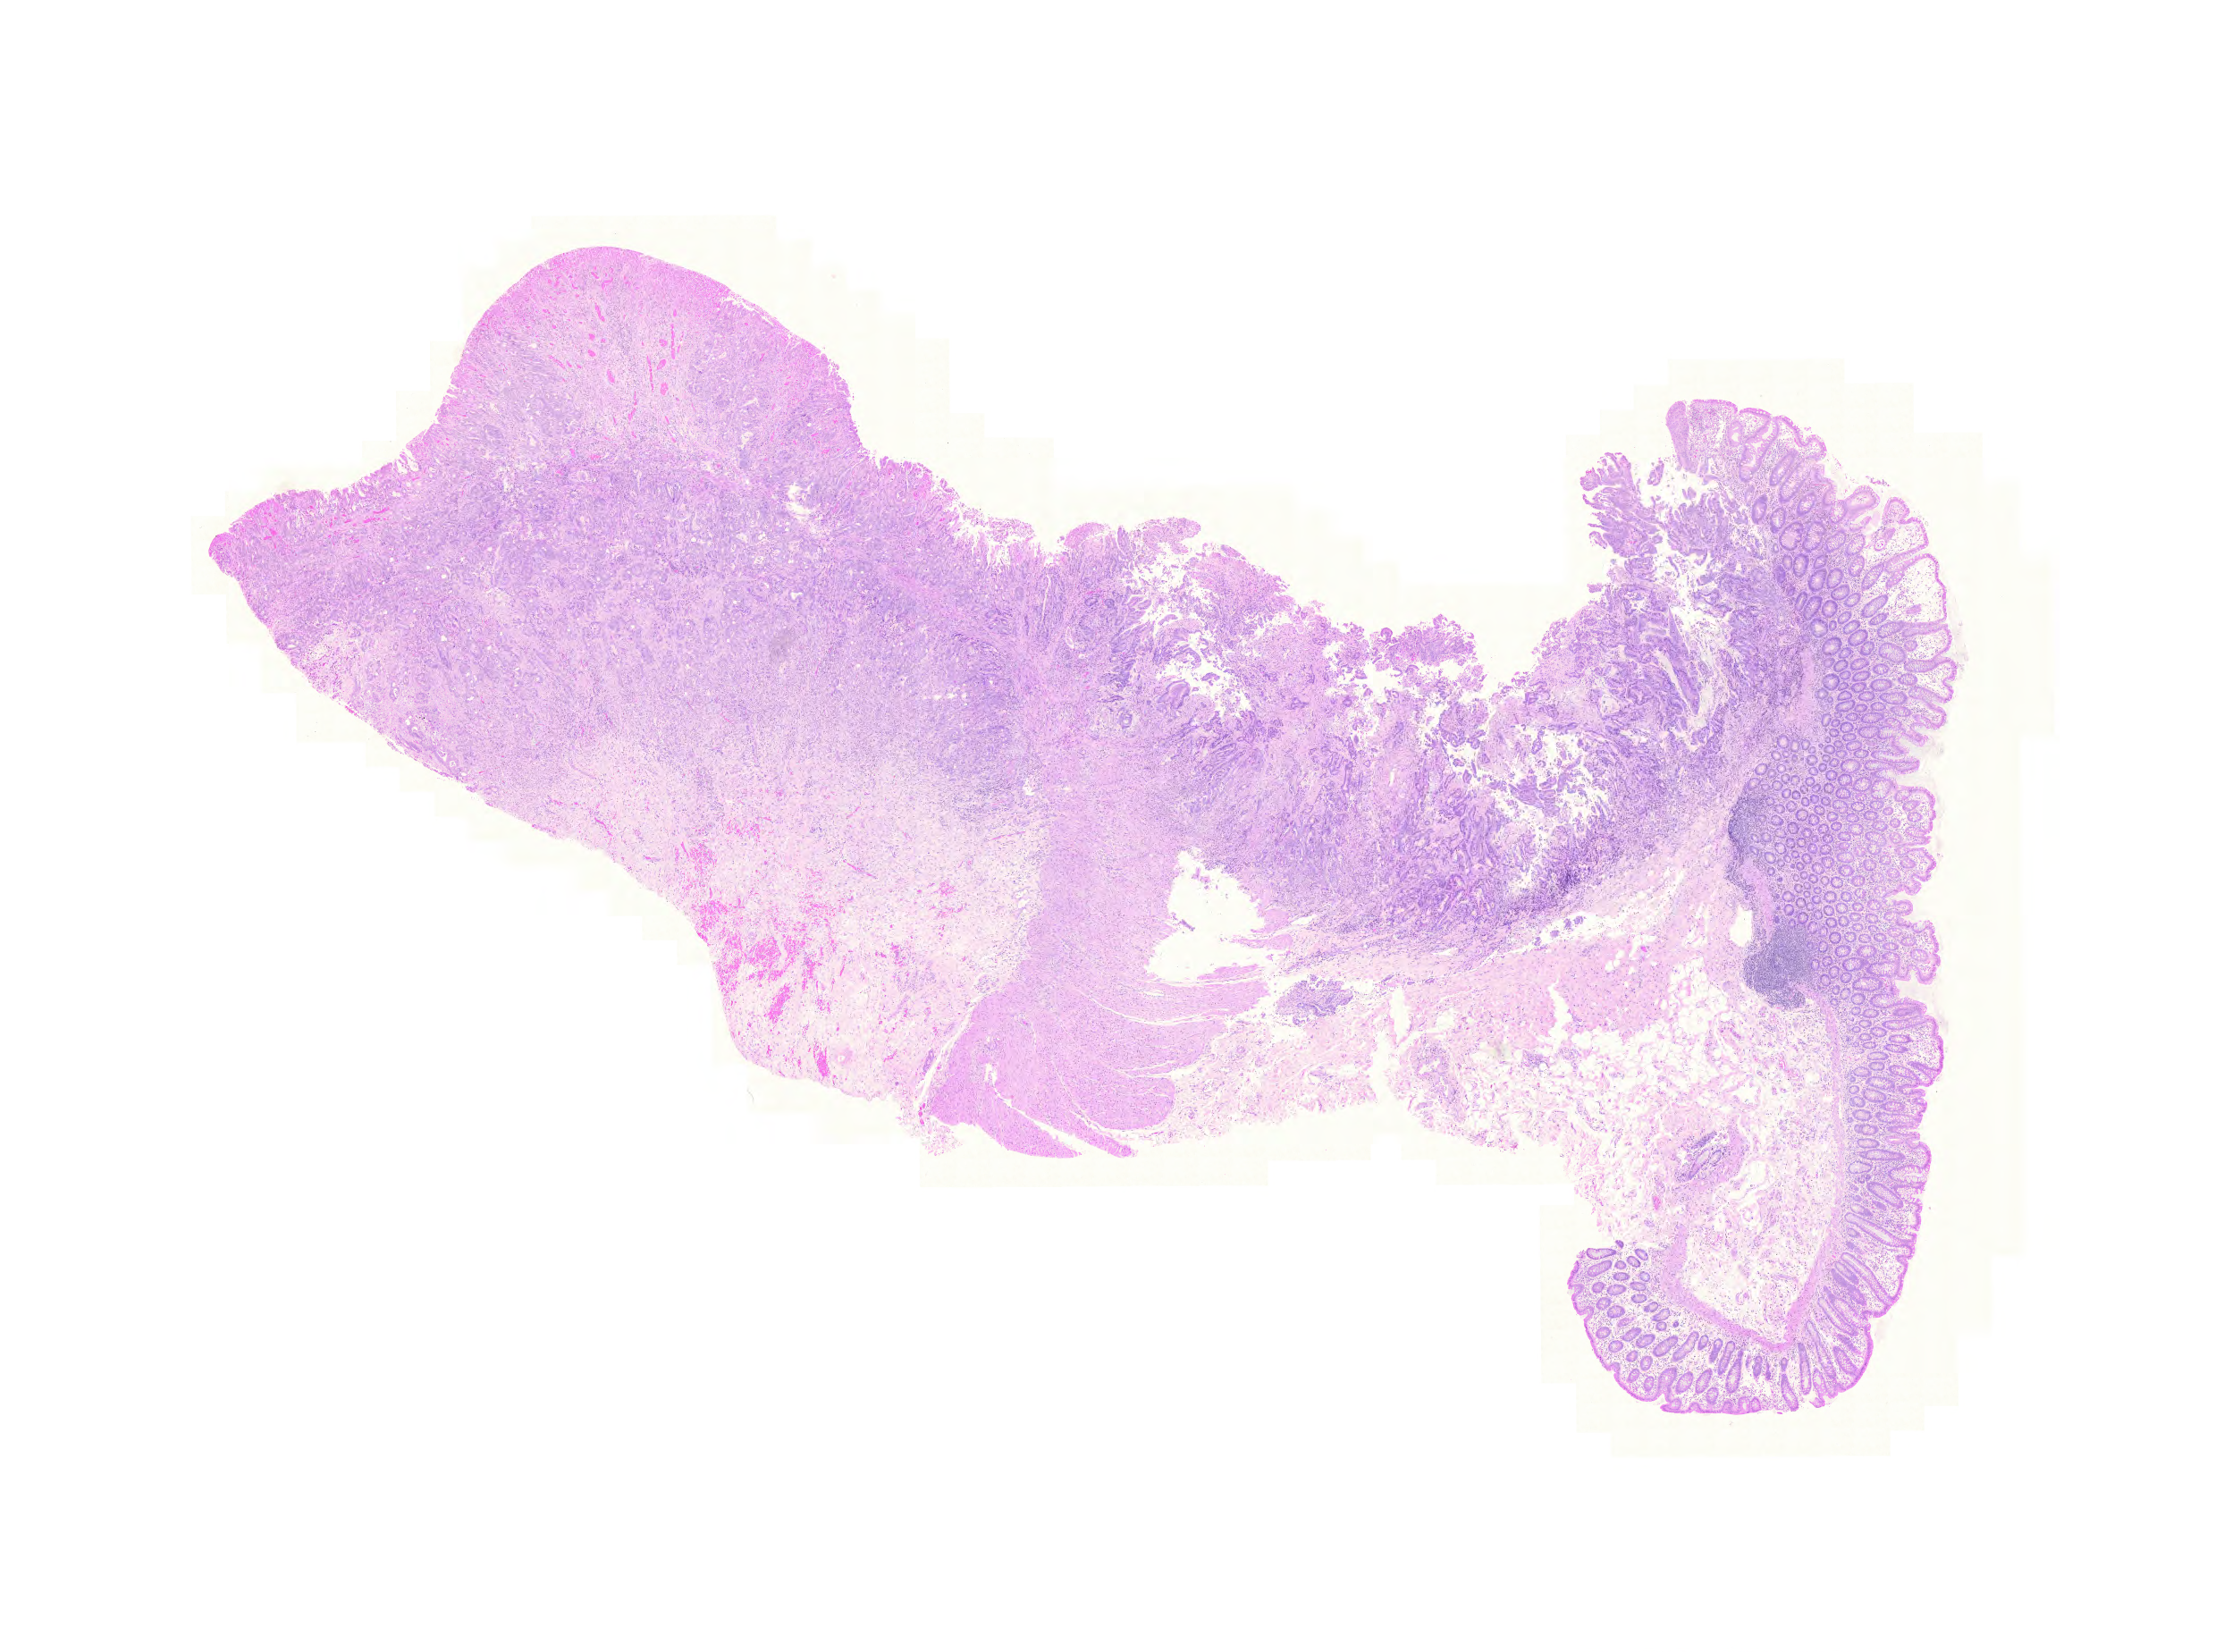
Whole-slide histology image, H&E, low-resolution overview of the scanned area, about 18.5 x 13.7 mm (acquisition: 20x scan); formalin-fixed paraffin-embedded (FFPE) diagnostic section; colon, primary tumour sample. Patient: female, age at initial diagnosis 63 years.
Diagnosis: Adenocarcinoma, NOS. AJCC pathologic stage: IIA. Lymph nodes positive (case pathology): 0 of 12 examined.